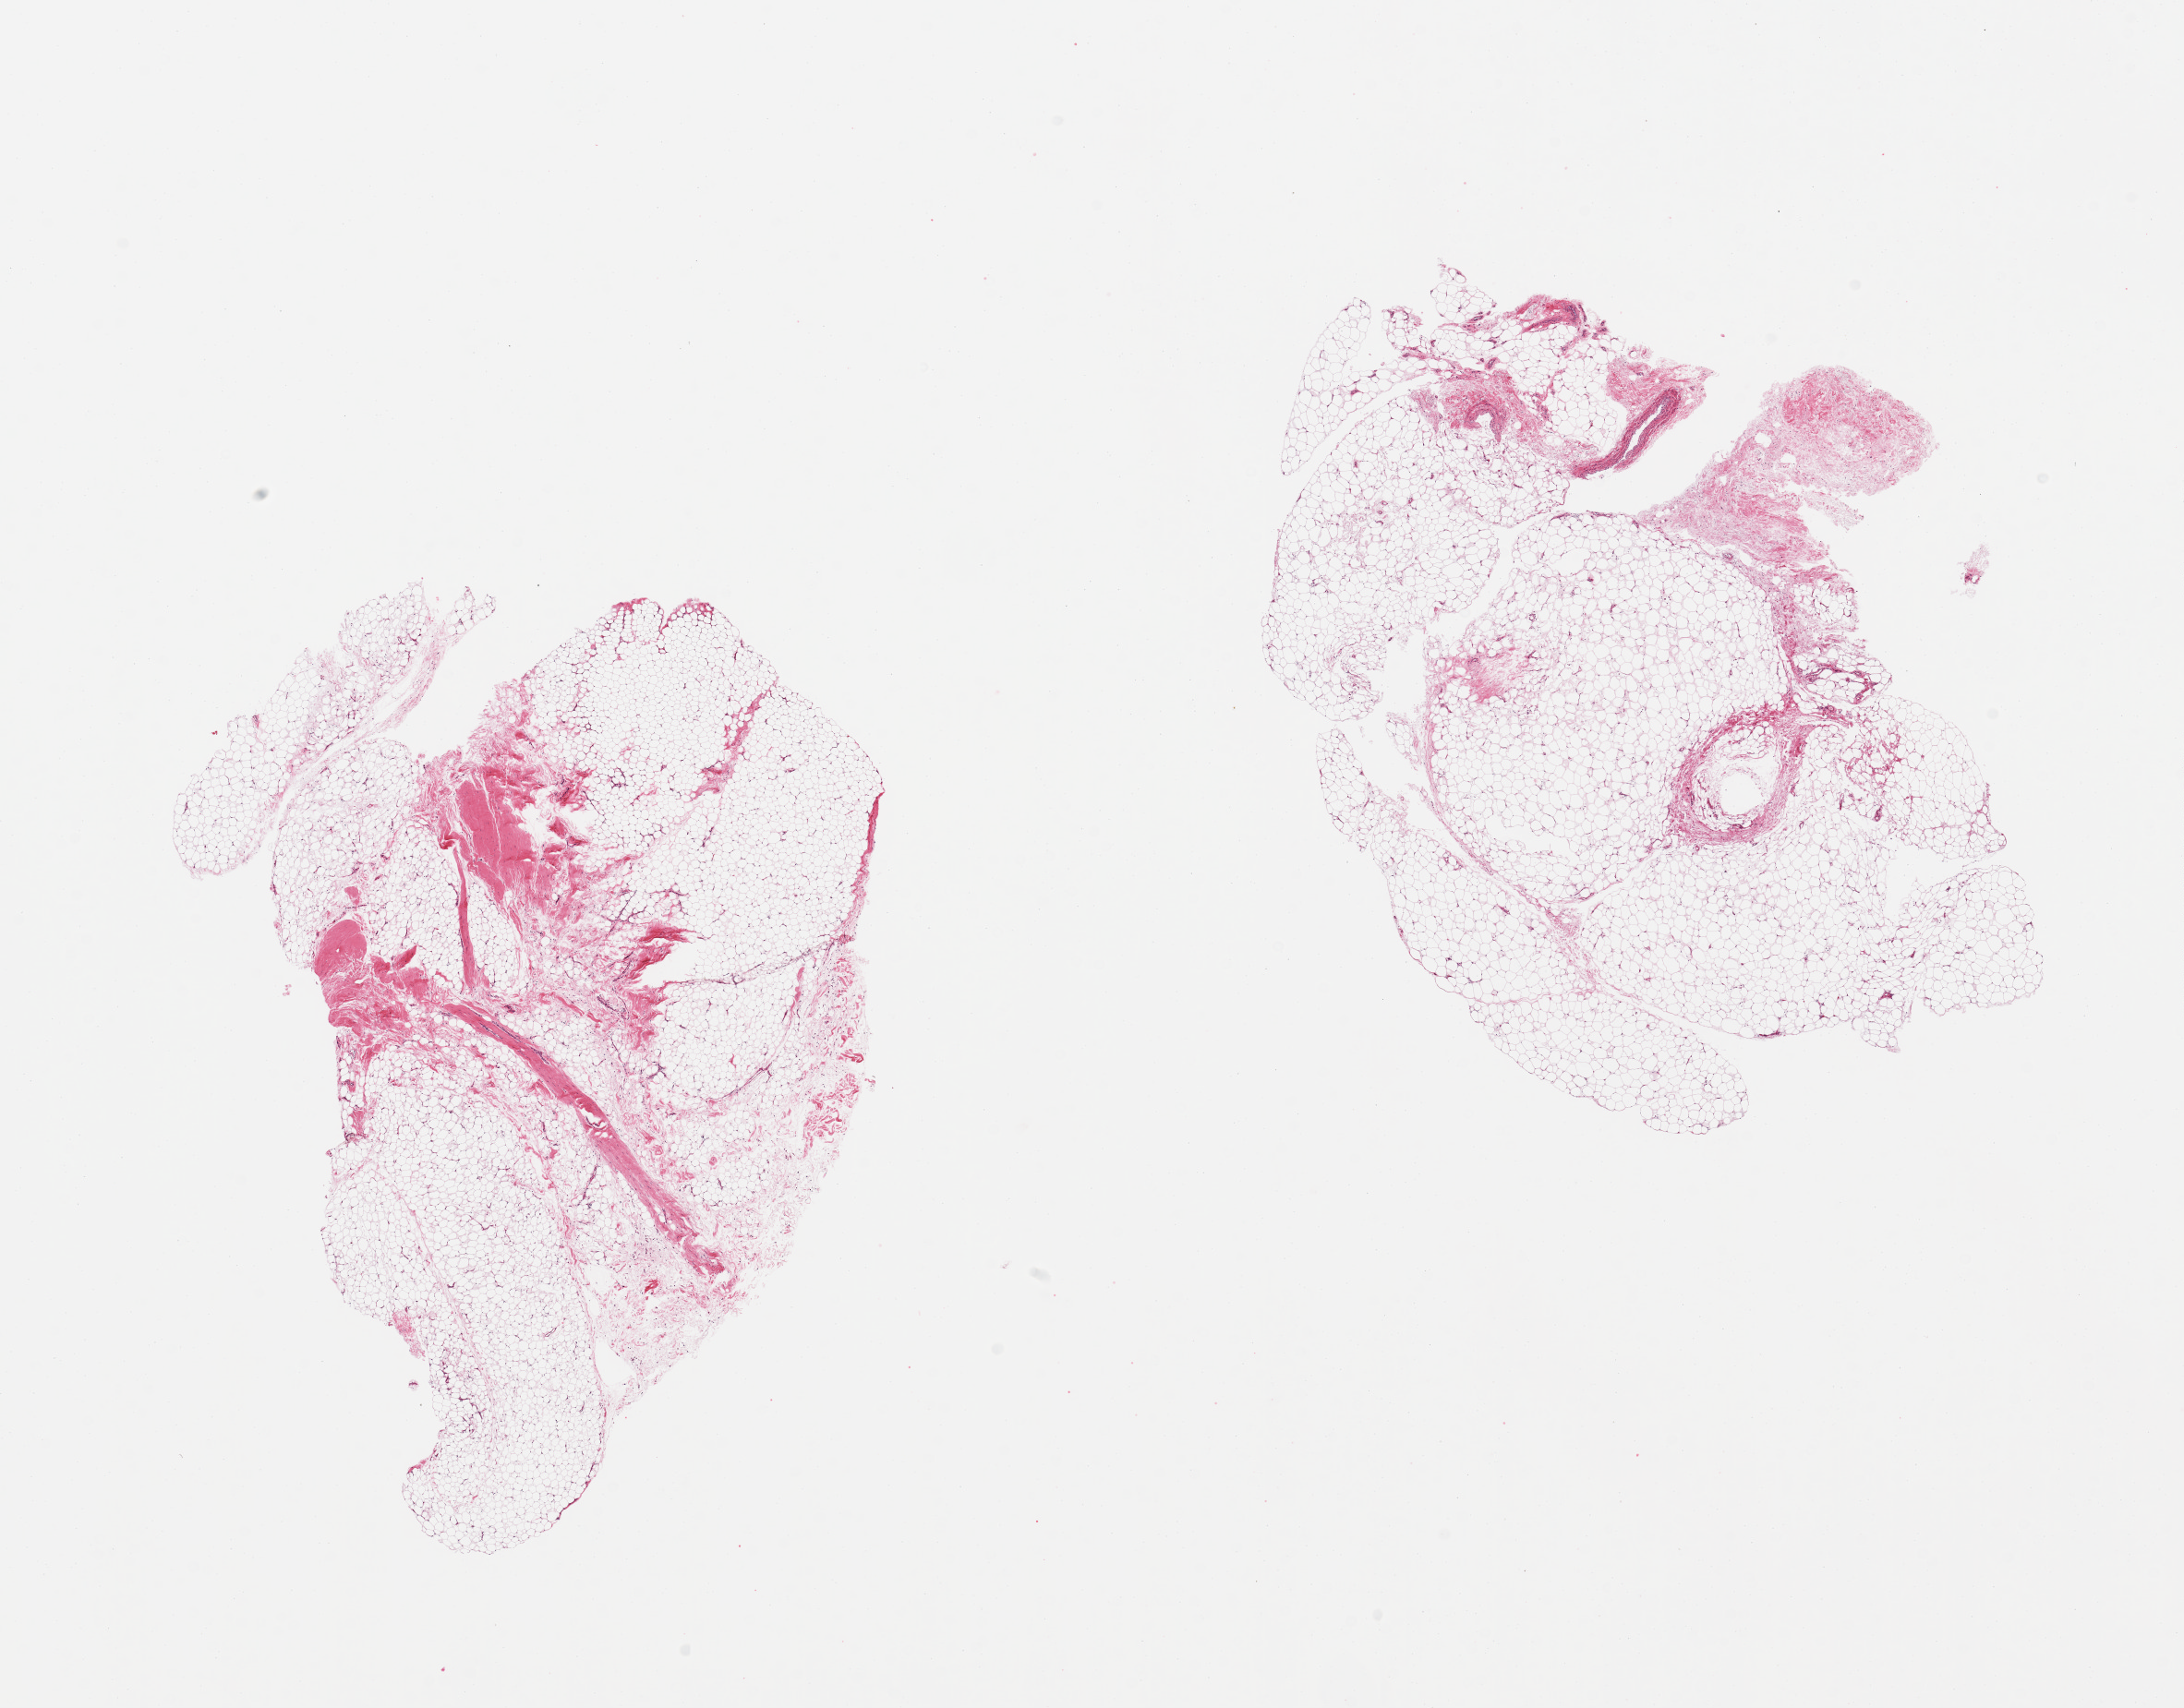
H&E whole-slide image, brightfield — a low-resolution overview of the entire scanned area, about 18.7 x 14.6 mm, PAXgene-fixed, paraffin-embedded tissue, section of adipose tissue (target tissue), donor tissue sample. Donor: male.
Reviewer comment on this tissue sample: 2 pieces; 10% fibrous content.